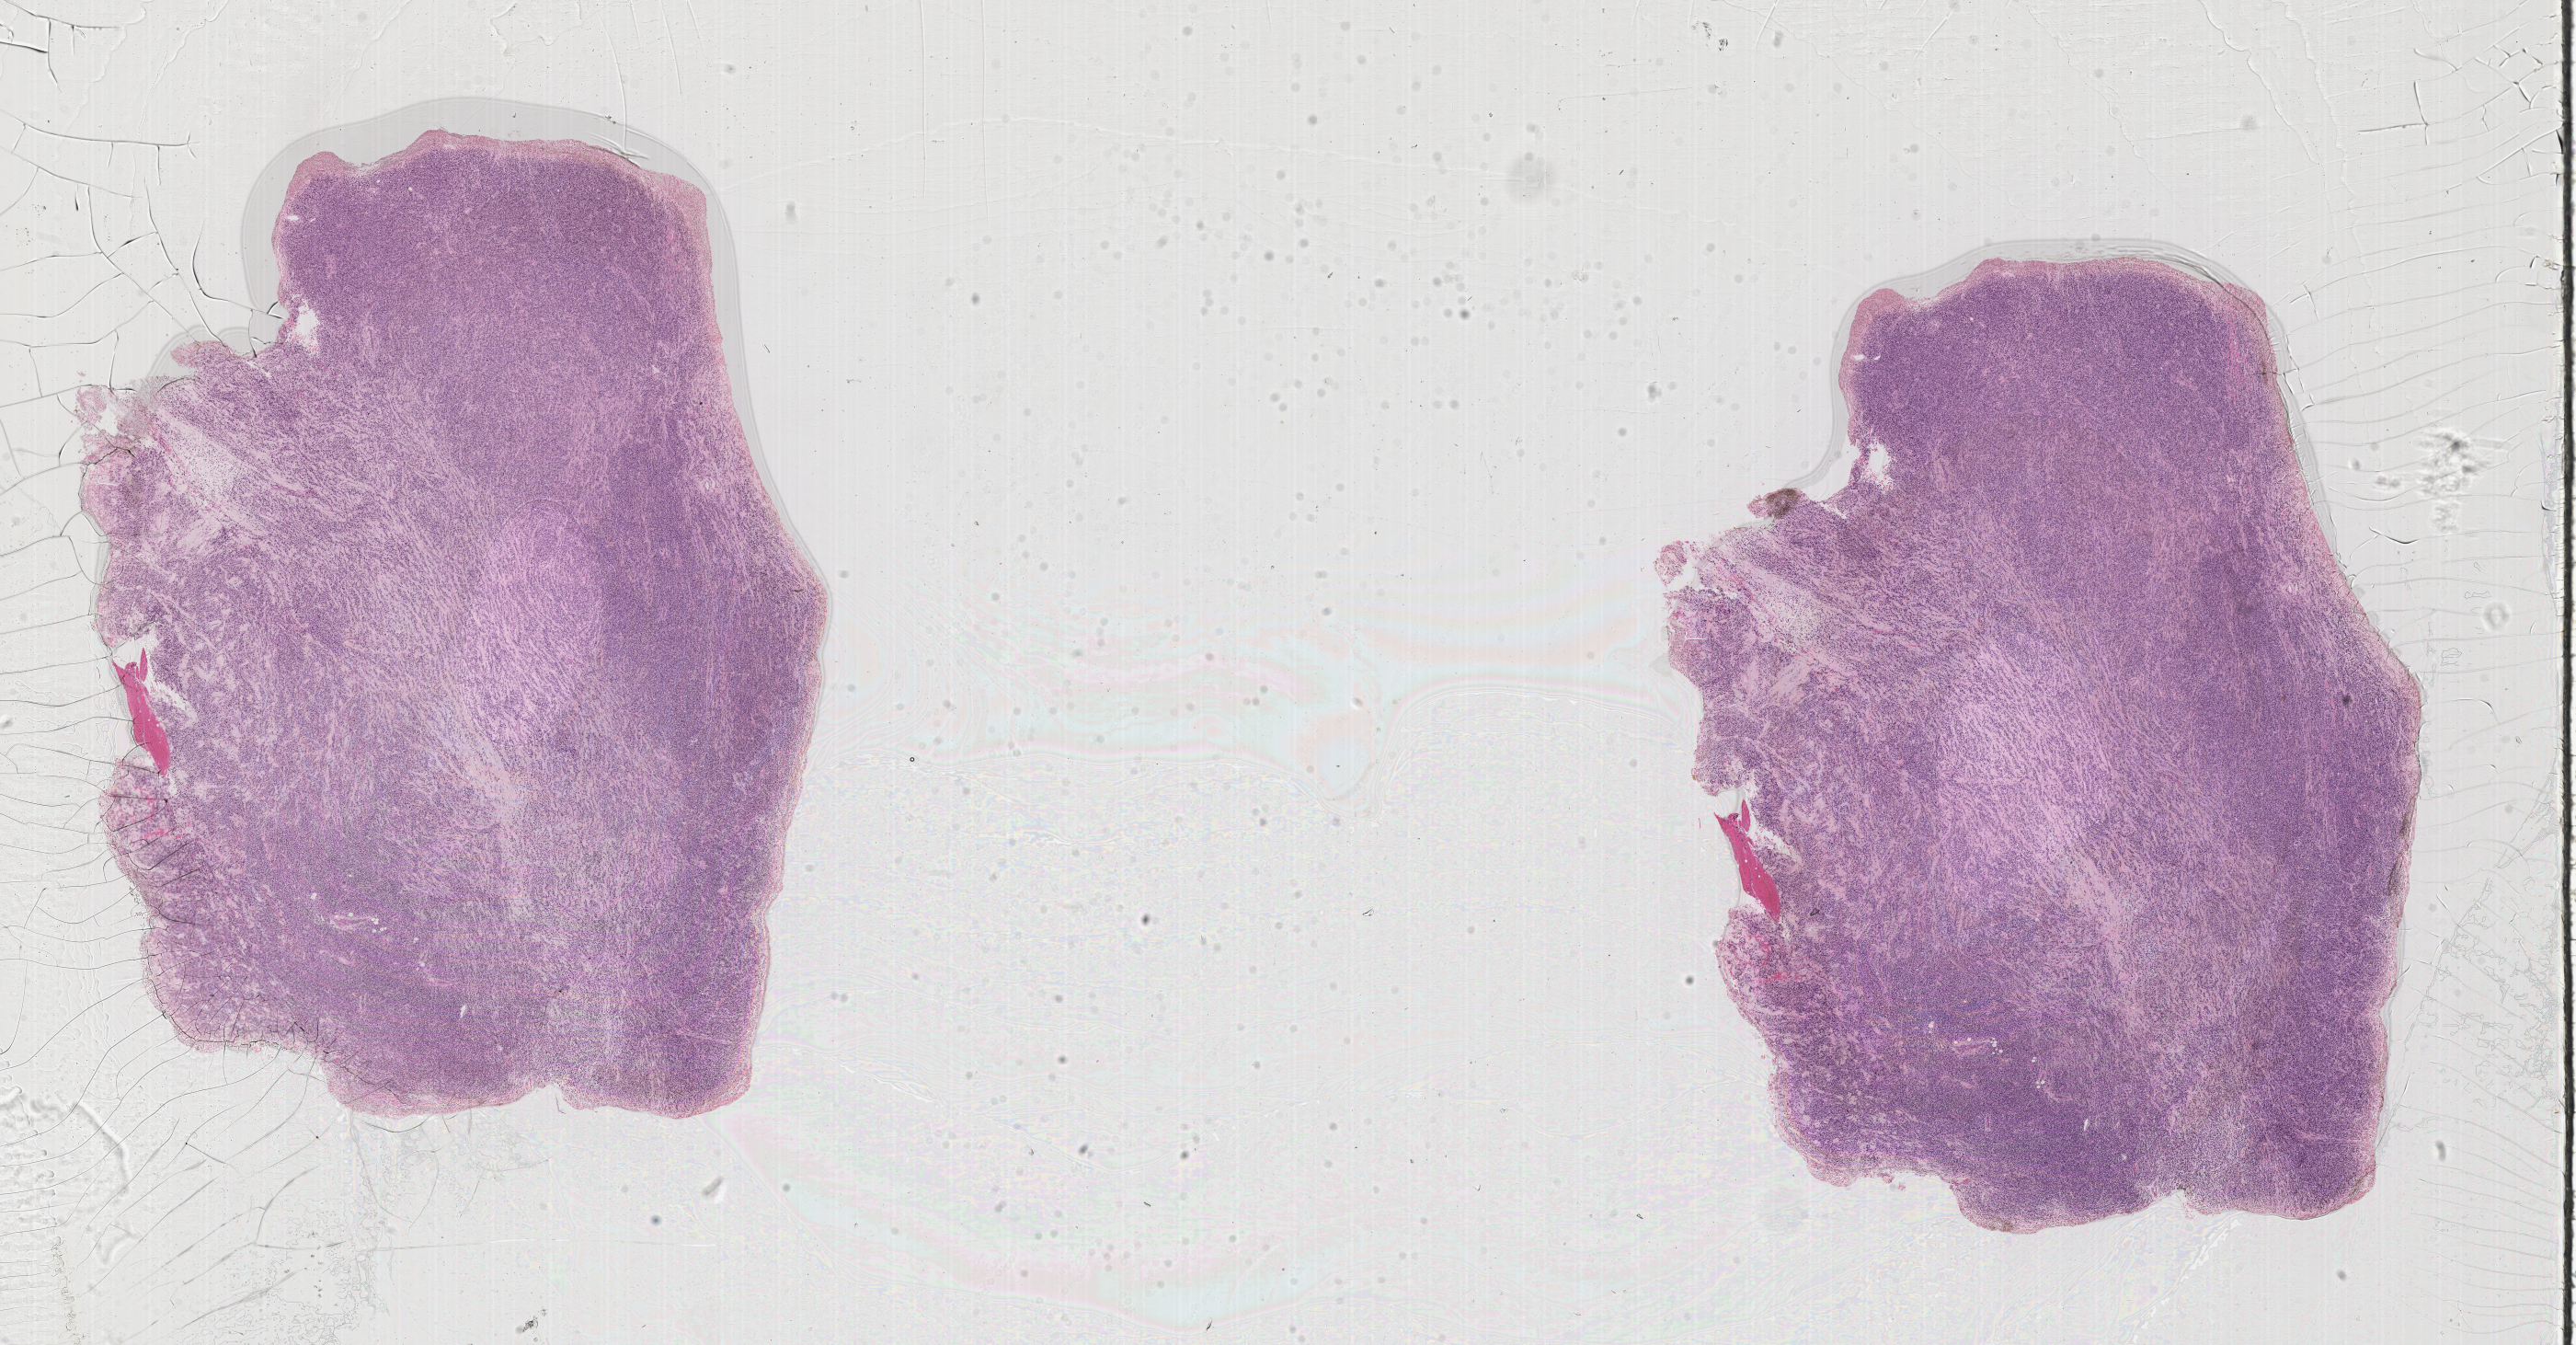
Whole-slide image, hematoxylin and eosin (H&E) stain of tumor tissue — whole scanned area (about 22.6 x 11.8 mm) shown as a low-resolution overview, FFPE section, site: soft tissue, buttock-right. Male patient, age at diagnosis 4.1 years.
Metastatic status at presentation (as recorded): non-metastatic. Stage (as recorded): 3. Diagnosis: rhabdomyosarcoma; histological classification: alveolar rhabdomyosarcoma.